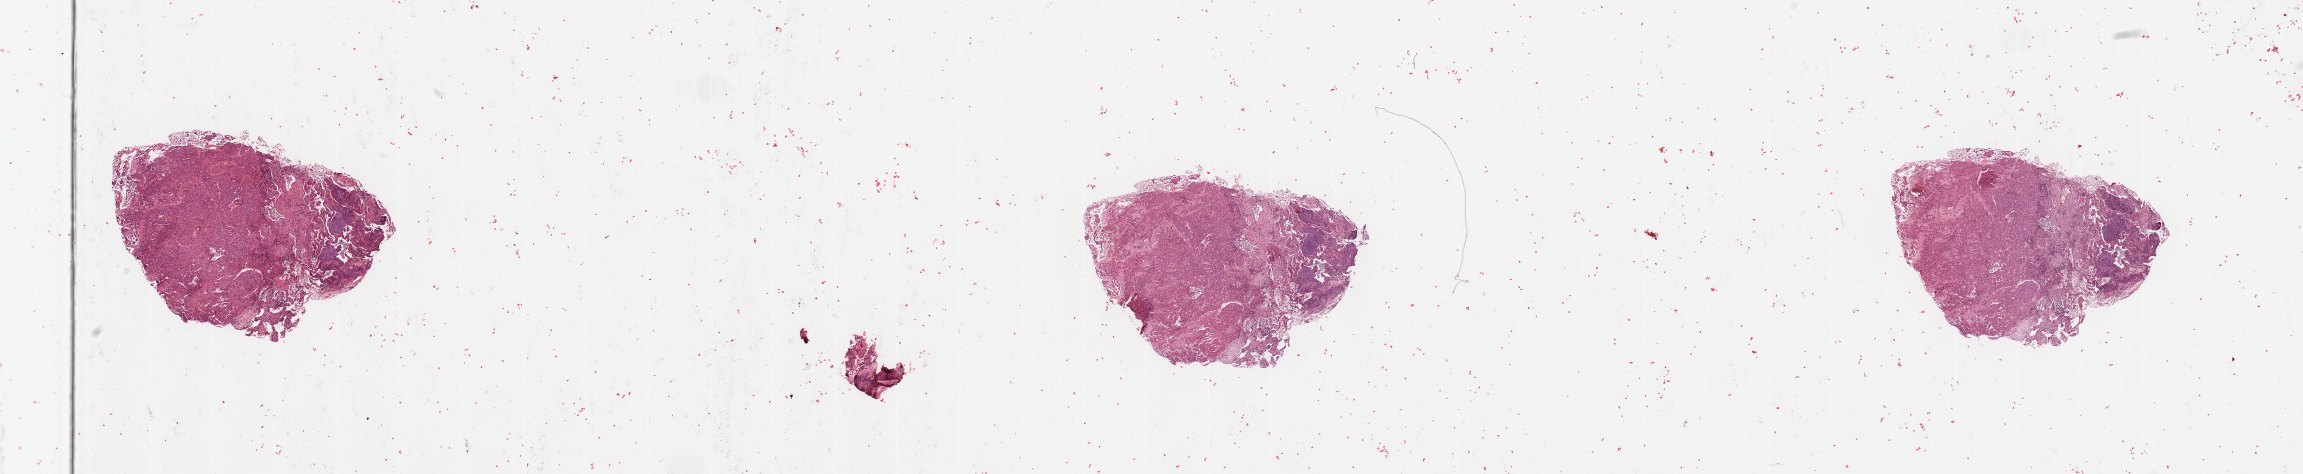
Whole-slide histology image, H&E, a low-resolution overview of the entire scanned area, about 36.4 x 7.5 mm (slide scanned at 20x); tumour tissue sample, sampled site: lung. 63-year-old female patient. Histologic grade: G1 (well differentiated). Slide review estimates, as recorded: tumour nuclei 60%, necrosis 2%.
• AJCC pathologic stage: IIA
• histologic diagnosis: Adenocarcinoma, NOS
• primary tumour site (as recorded): left upper lobe